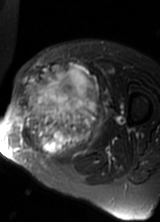
MRI of an extremity soft-tissue mass, one axial slice. Position 37 of 69 along the scan axis. T2-weighted fat-saturated. MR volume resampled by the dataset authors to the PET/CT grid (not the native acquisition matrix). 160 × 222 image matrix, field of view 156 × 217 mm. Female patient. Case-level facts recorded for this patient, not image findings: histological type: pleomorphic leiomyosarcoma; grade: high; site of the primary tumour: left thigh.
Outlined on this slice (expert contour drawn on MRI and transferred to this co-registered scan by the dataset authors):
- gross tumour volume including surrounding oedema: box from (x=18, y=63) to (x=106, y=160) px
- gross tumour volume (mass): (x=18, y=63)–(x=101, y=158)